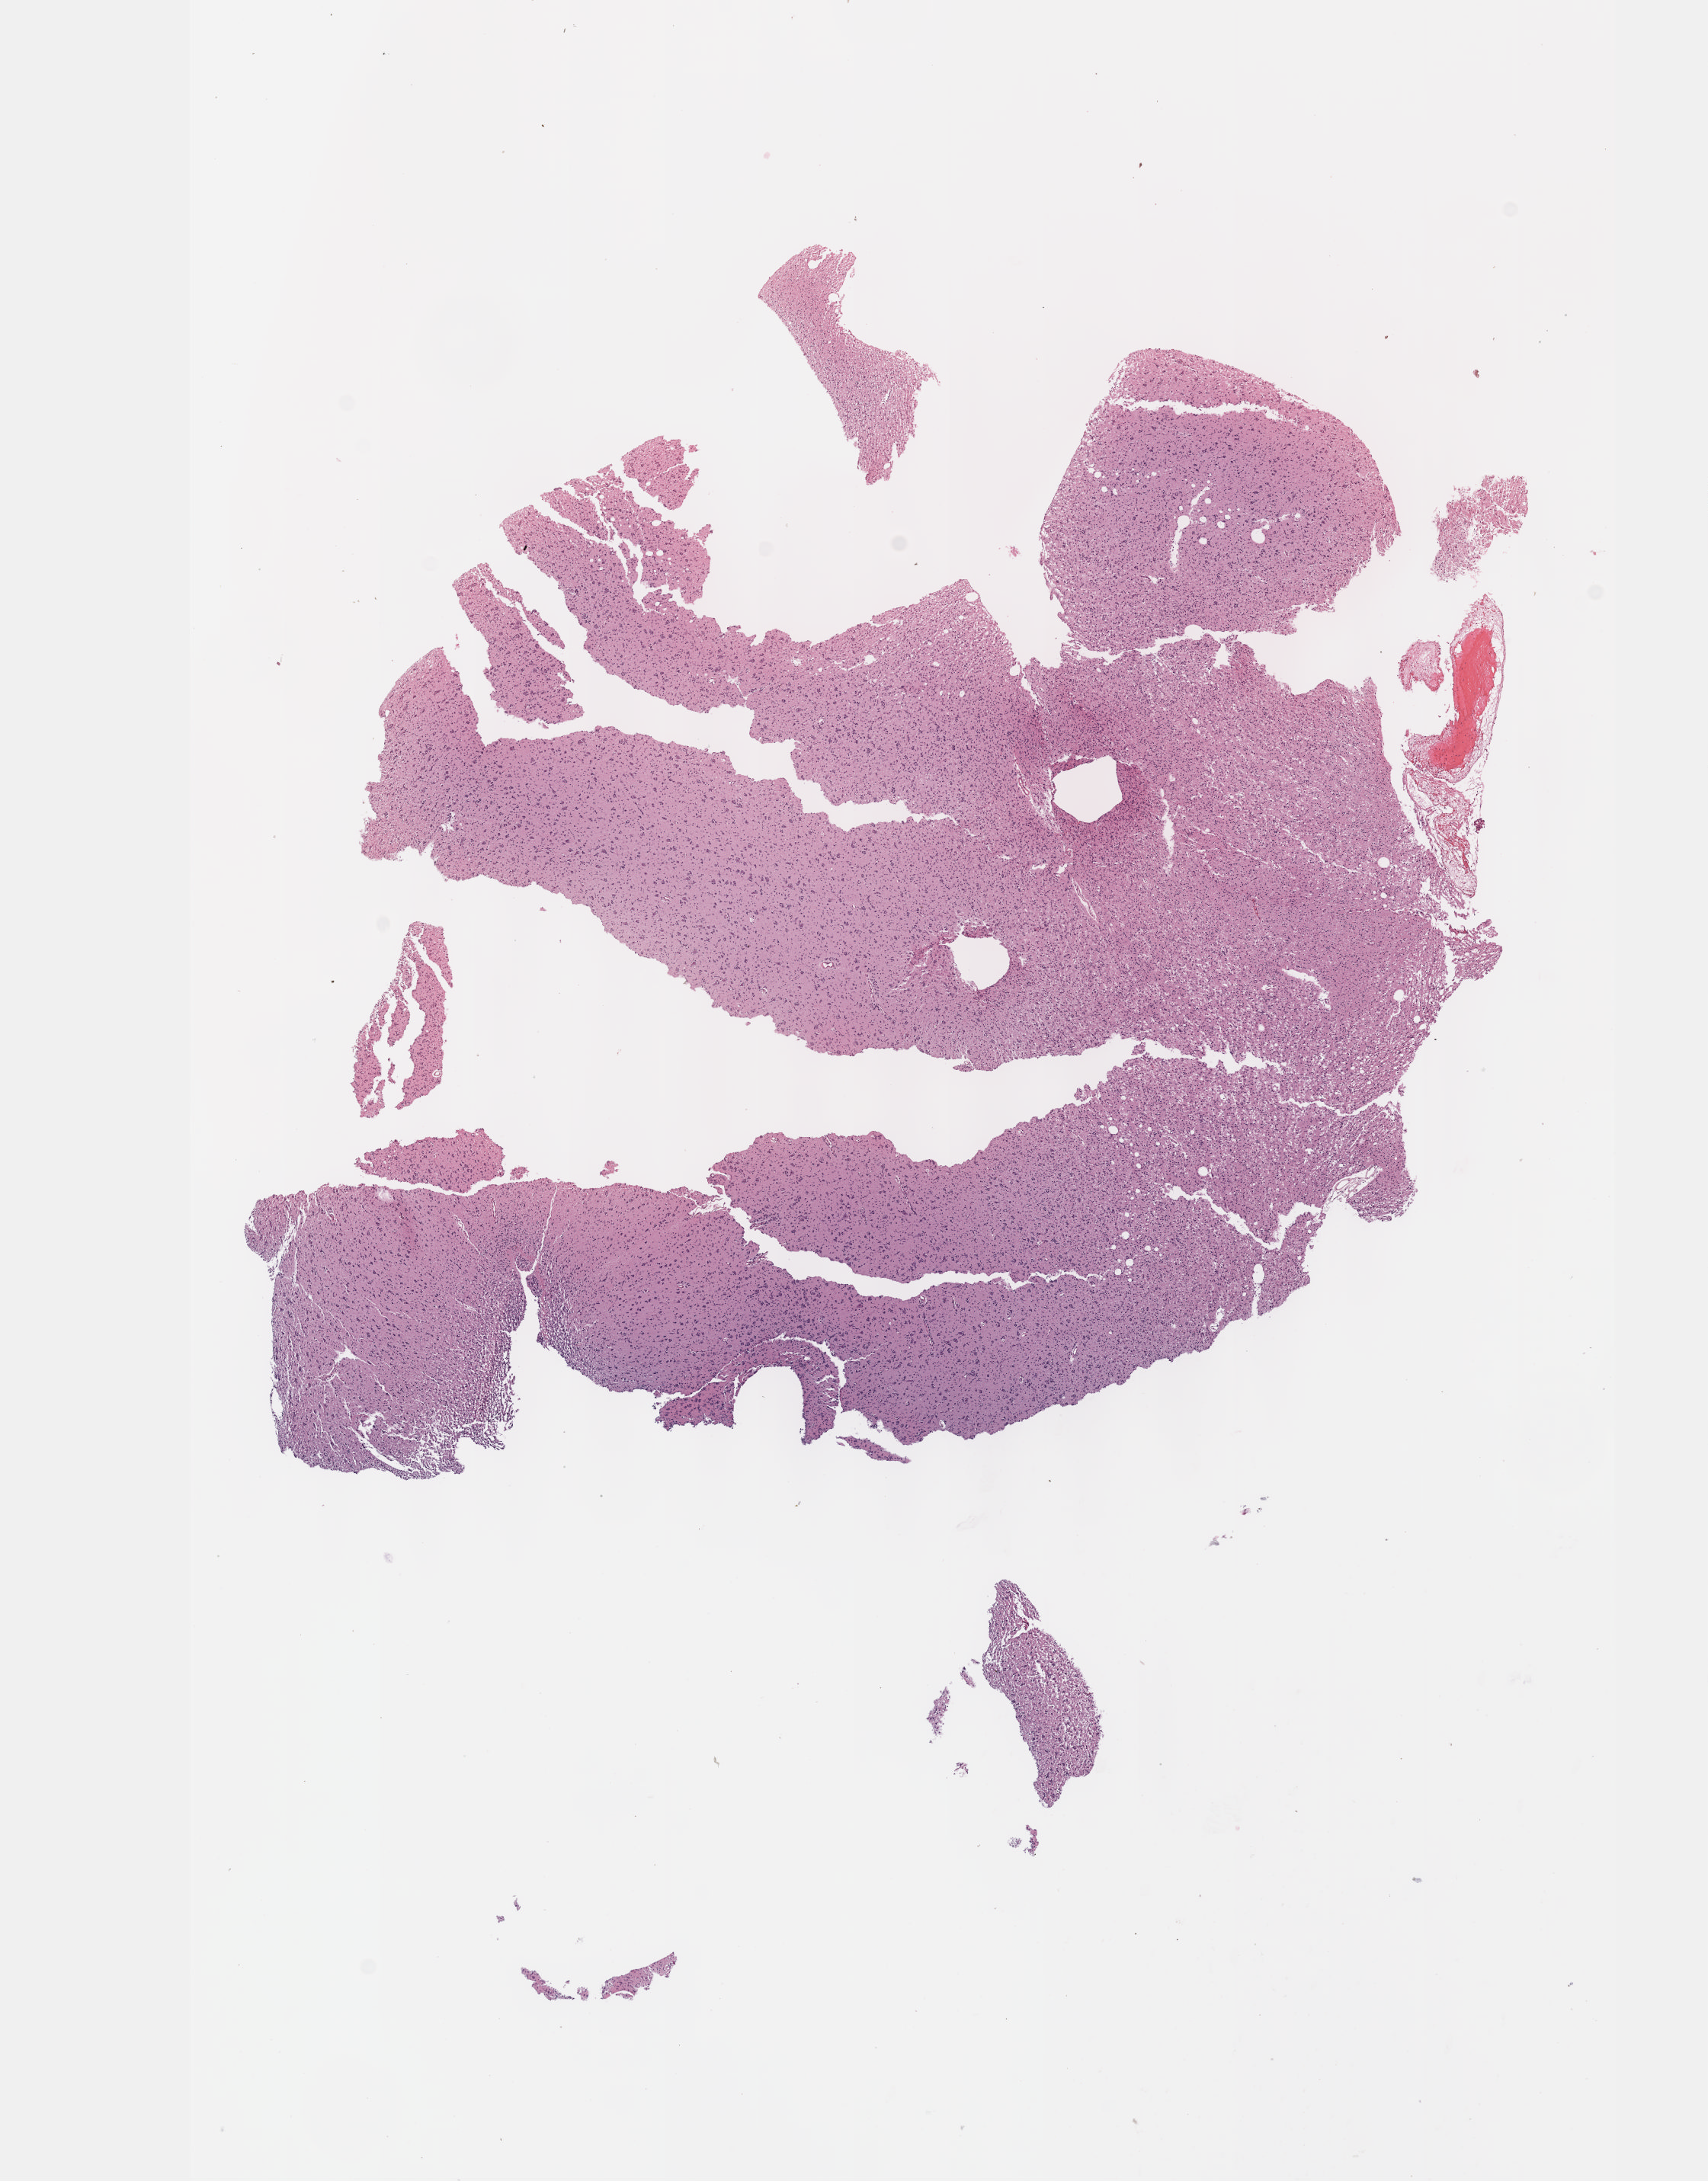
H&E-stained whole-slide image, whole scanned area (about 9.1 x 11.6 mm, acquisition: 40x scan) shown as a low-resolution overview. FFPE section. Sample: primary tumour, brain. Female, age 32 years at initial diagnosis. Histologic grade: G2 (moderately differentiated).
Laterality: left. Pathologic diagnosis: Oligodendroglioma, NOS.